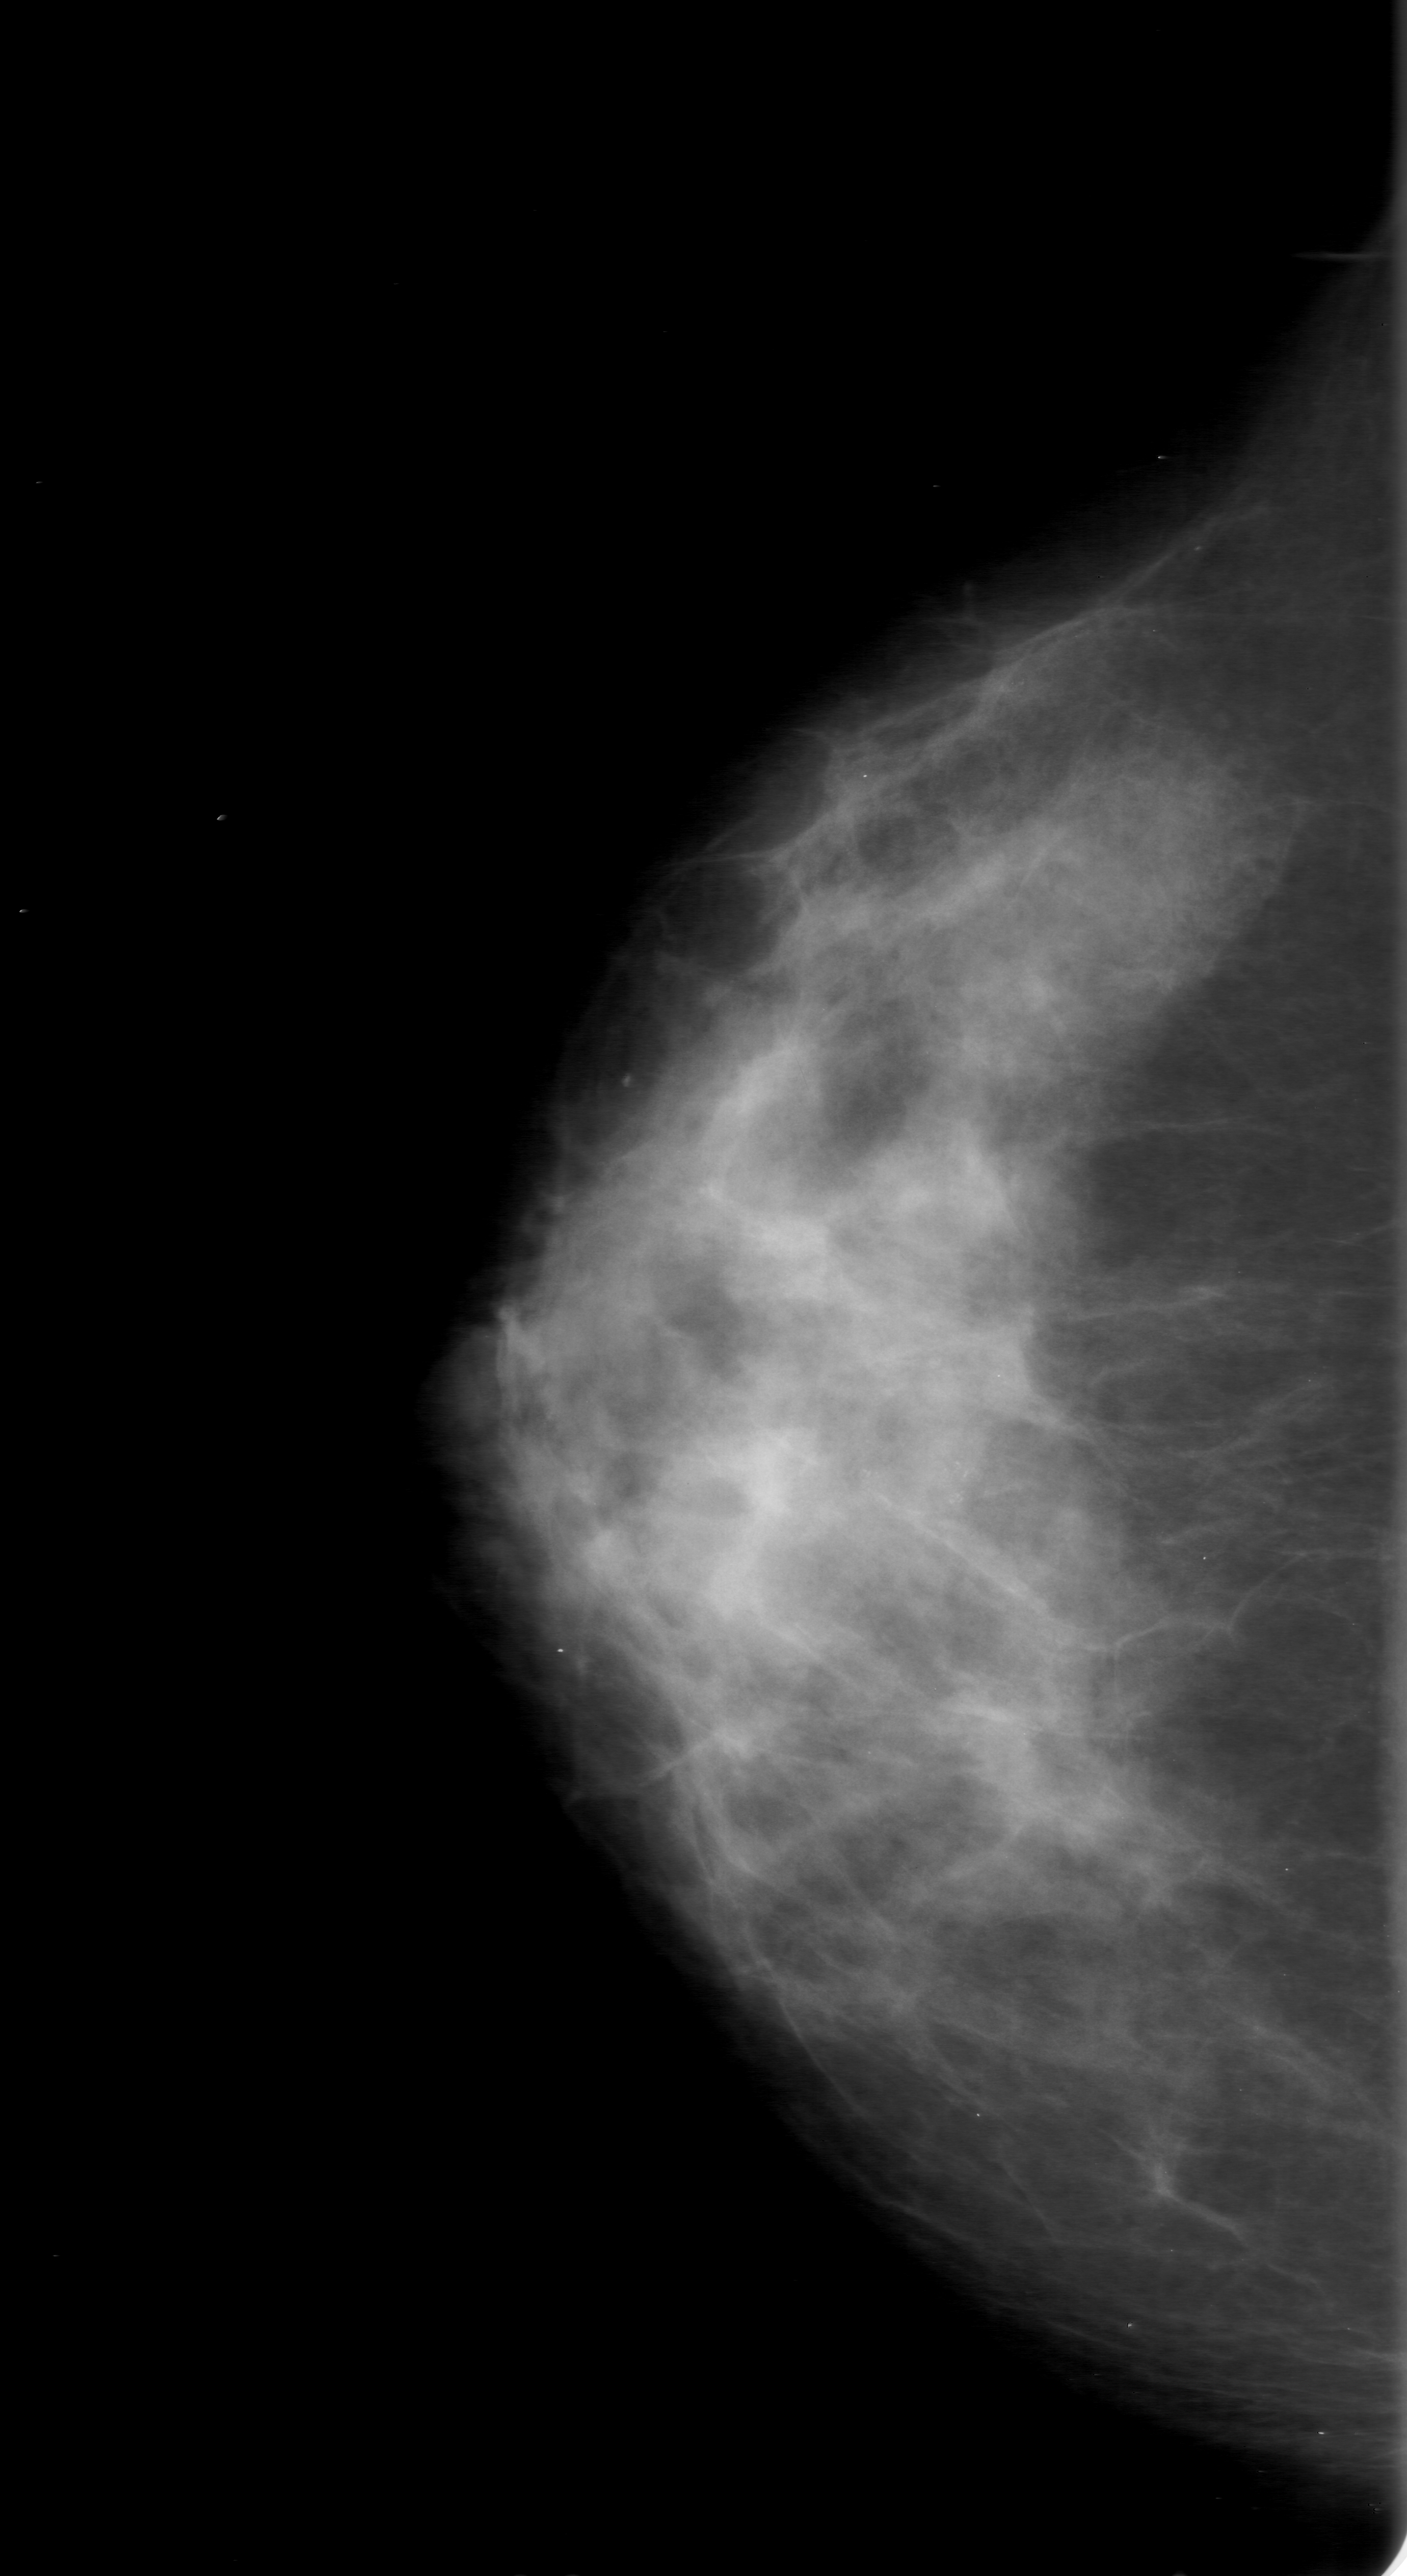
Scanned film-screen mammogram; right breast; CC view; breast composition: heterogeneously dense (BI-RADS density category 3 of 4).
- Abnormality record for this image: calcifications, morphology amorphous, distribution clustered; BI-RADS assessment category 3; pathology (as recorded): malignant.